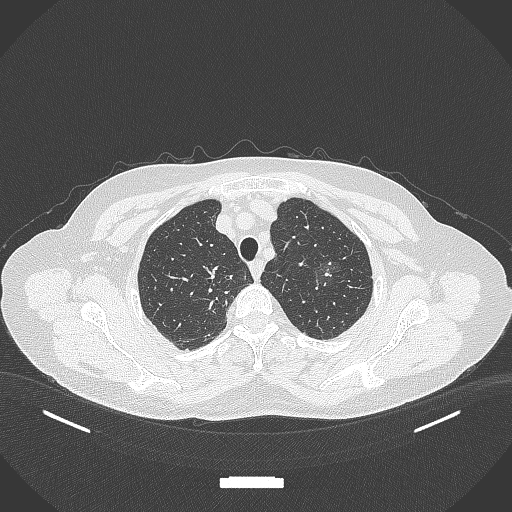
Chest CT, one axial slice; slice 299 of 369 in the series (ordered by position); lung window (W 1500 / L -600 HU); 1 mm slice thickness; 512 × 512 image matrix, field of view 400 × 400 mm. Female patient, age 64 years. From the clinical record (not read from this slice): clinical TNM (as recorded): T1c N0 M0; histopathological grade: G1.
Structures marked on this image (bounding box drawn by a radiologist):
- lung tumour (recorded histology: adenocarcinoma): bounding box <304,250,344,294> (left, top, right, bottom; pixels)